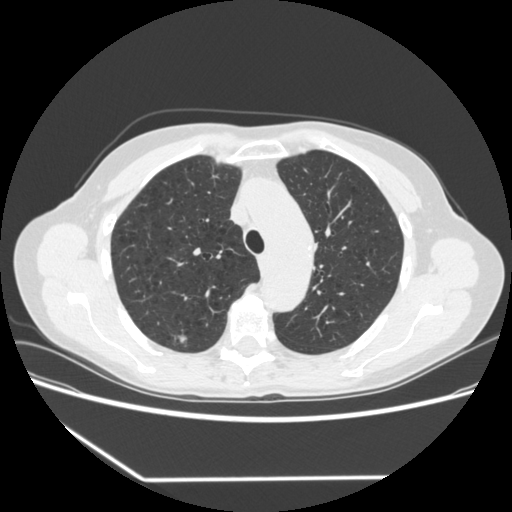
Axial slice from a low-dose chest CT screening exam; baseline screening round; lung window (W 1500 / L -600 HU); 1.25 mm slice thickness; standard (soft-tissue) reconstruction kernel (STANDARD); slice 249 of 323 in the series. Female participant, aged 67 years at enrolment. Current smoker at enrolment.
Expert-annotated lung lesion, bounding box [x1, y1, x2, y2] px = [152, 321, 199, 356]. The screening reader recorded 2 non-calcified nodules or masses ≥4 mm on this exam (right upper lobe, right lower lobe); which of them this box marks is not recorded. Lung cancer was diagnosed 29 days after this screen: adenocarcinoma, NOS, right upper lobe, moderately differentiated (G2), stage IA (AJCC 6th edition), 24 mm at pathology.